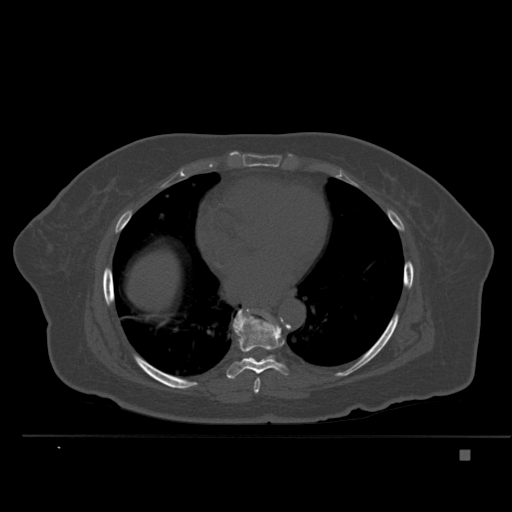
CT including the spine, one axial slice. Bone window (W 1800 / L 400 HU). 1.5 mm slice thickness. 512 × 512 image matrix. Patient: female, 74 years. Case-level facts recorded for this patient, not image findings: primary cancer: colon.
Annotated regions visible in this slice (semi-automatically segmented with operator editing):
- T7 vertebra: bounding box <254,378,260,393> (left, top, right, bottom; pixels)
- T8 vertebra: <227,309,288,379>
- T9 vertebra: <250,311,274,360>